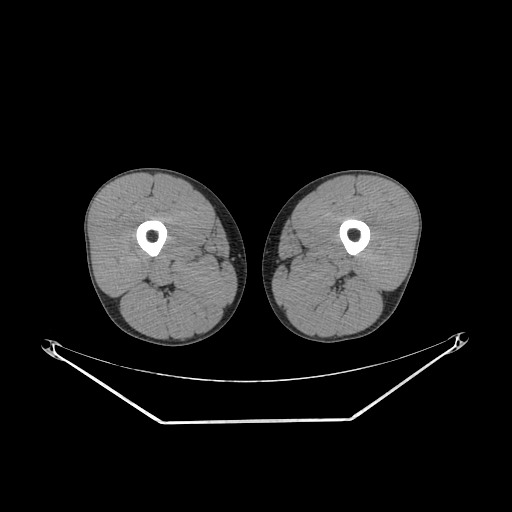
CT of an extremity soft-tissue mass (from a PET/CT study), one axial slice; slice 219 of 267 in the series (ordered by position); 140 kVp; soft-tissue window (W 400 / L 40 HU); 3.75 mm slice thickness; 512 × 512 image matrix, field of view 500 × 500 mm. Male patient. Case-level facts recorded for this patient, not image findings: histological type: extraskeletal osteosarcoma; grade: high; site of the primary tumour: left adductur.
Structures marked on this image (expert contour drawn on MRI and transferred to this co-registered scan by the dataset authors):
- gross tumour volume (mass): box from (x=283, y=251) to (x=357, y=280) px